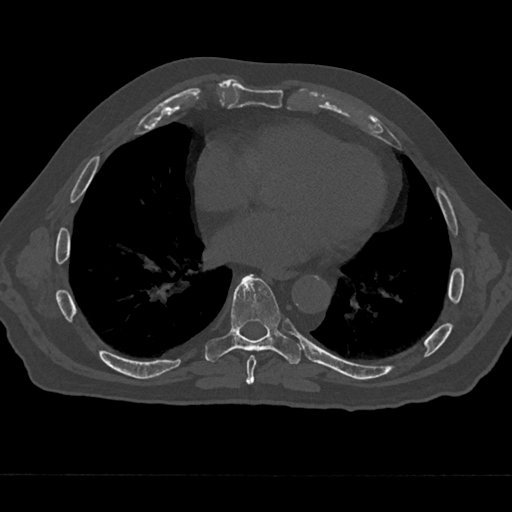
CT including the spine, one axial slice; slice 327 of 797 in the series (ordered by position); reconstruction kernel Br40s/3; bone window (W 1800 / L 400 HU); 512 × 512 image matrix, field of view 377 × 377 mm. Patient: male, 75 years. From the clinical record (not read from this slice): primary cancer: renal; vertebrae with lytic lesions (as recorded): T4.
Structures marked on this image (semi-automatic segmentation, software-assisted and operator-edited):
- T7 vertebra: bounding box (x1, y1, x2, y2) in pixels: (243, 355, 257, 385)
- T8 vertebra: (204, 274, 301, 364)